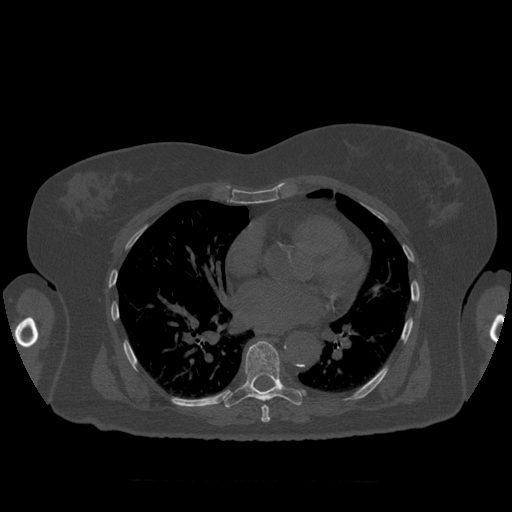
CT including the spine, one axial slice; position 381 of 399 along the scan axis; reconstruction kernel STANDARD; 120 kVp; bone window (W 1800 / L 400 HU); 1.25 mm slice thickness; 512 × 512 image matrix, field of view 404 × 404 mm. Patient age 81 years. Case-level facts recorded for this patient, not image findings: primary cancer: renal; vertebrae with lytic lesions (as recorded): L1.
Structures marked on this image (semi-automatically segmented with operator editing):
- T7 vertebra: bounding box (x1, y1, x2, y2) in pixels: (261, 404, 270, 423)
- T8 vertebra: (223, 341, 303, 408)